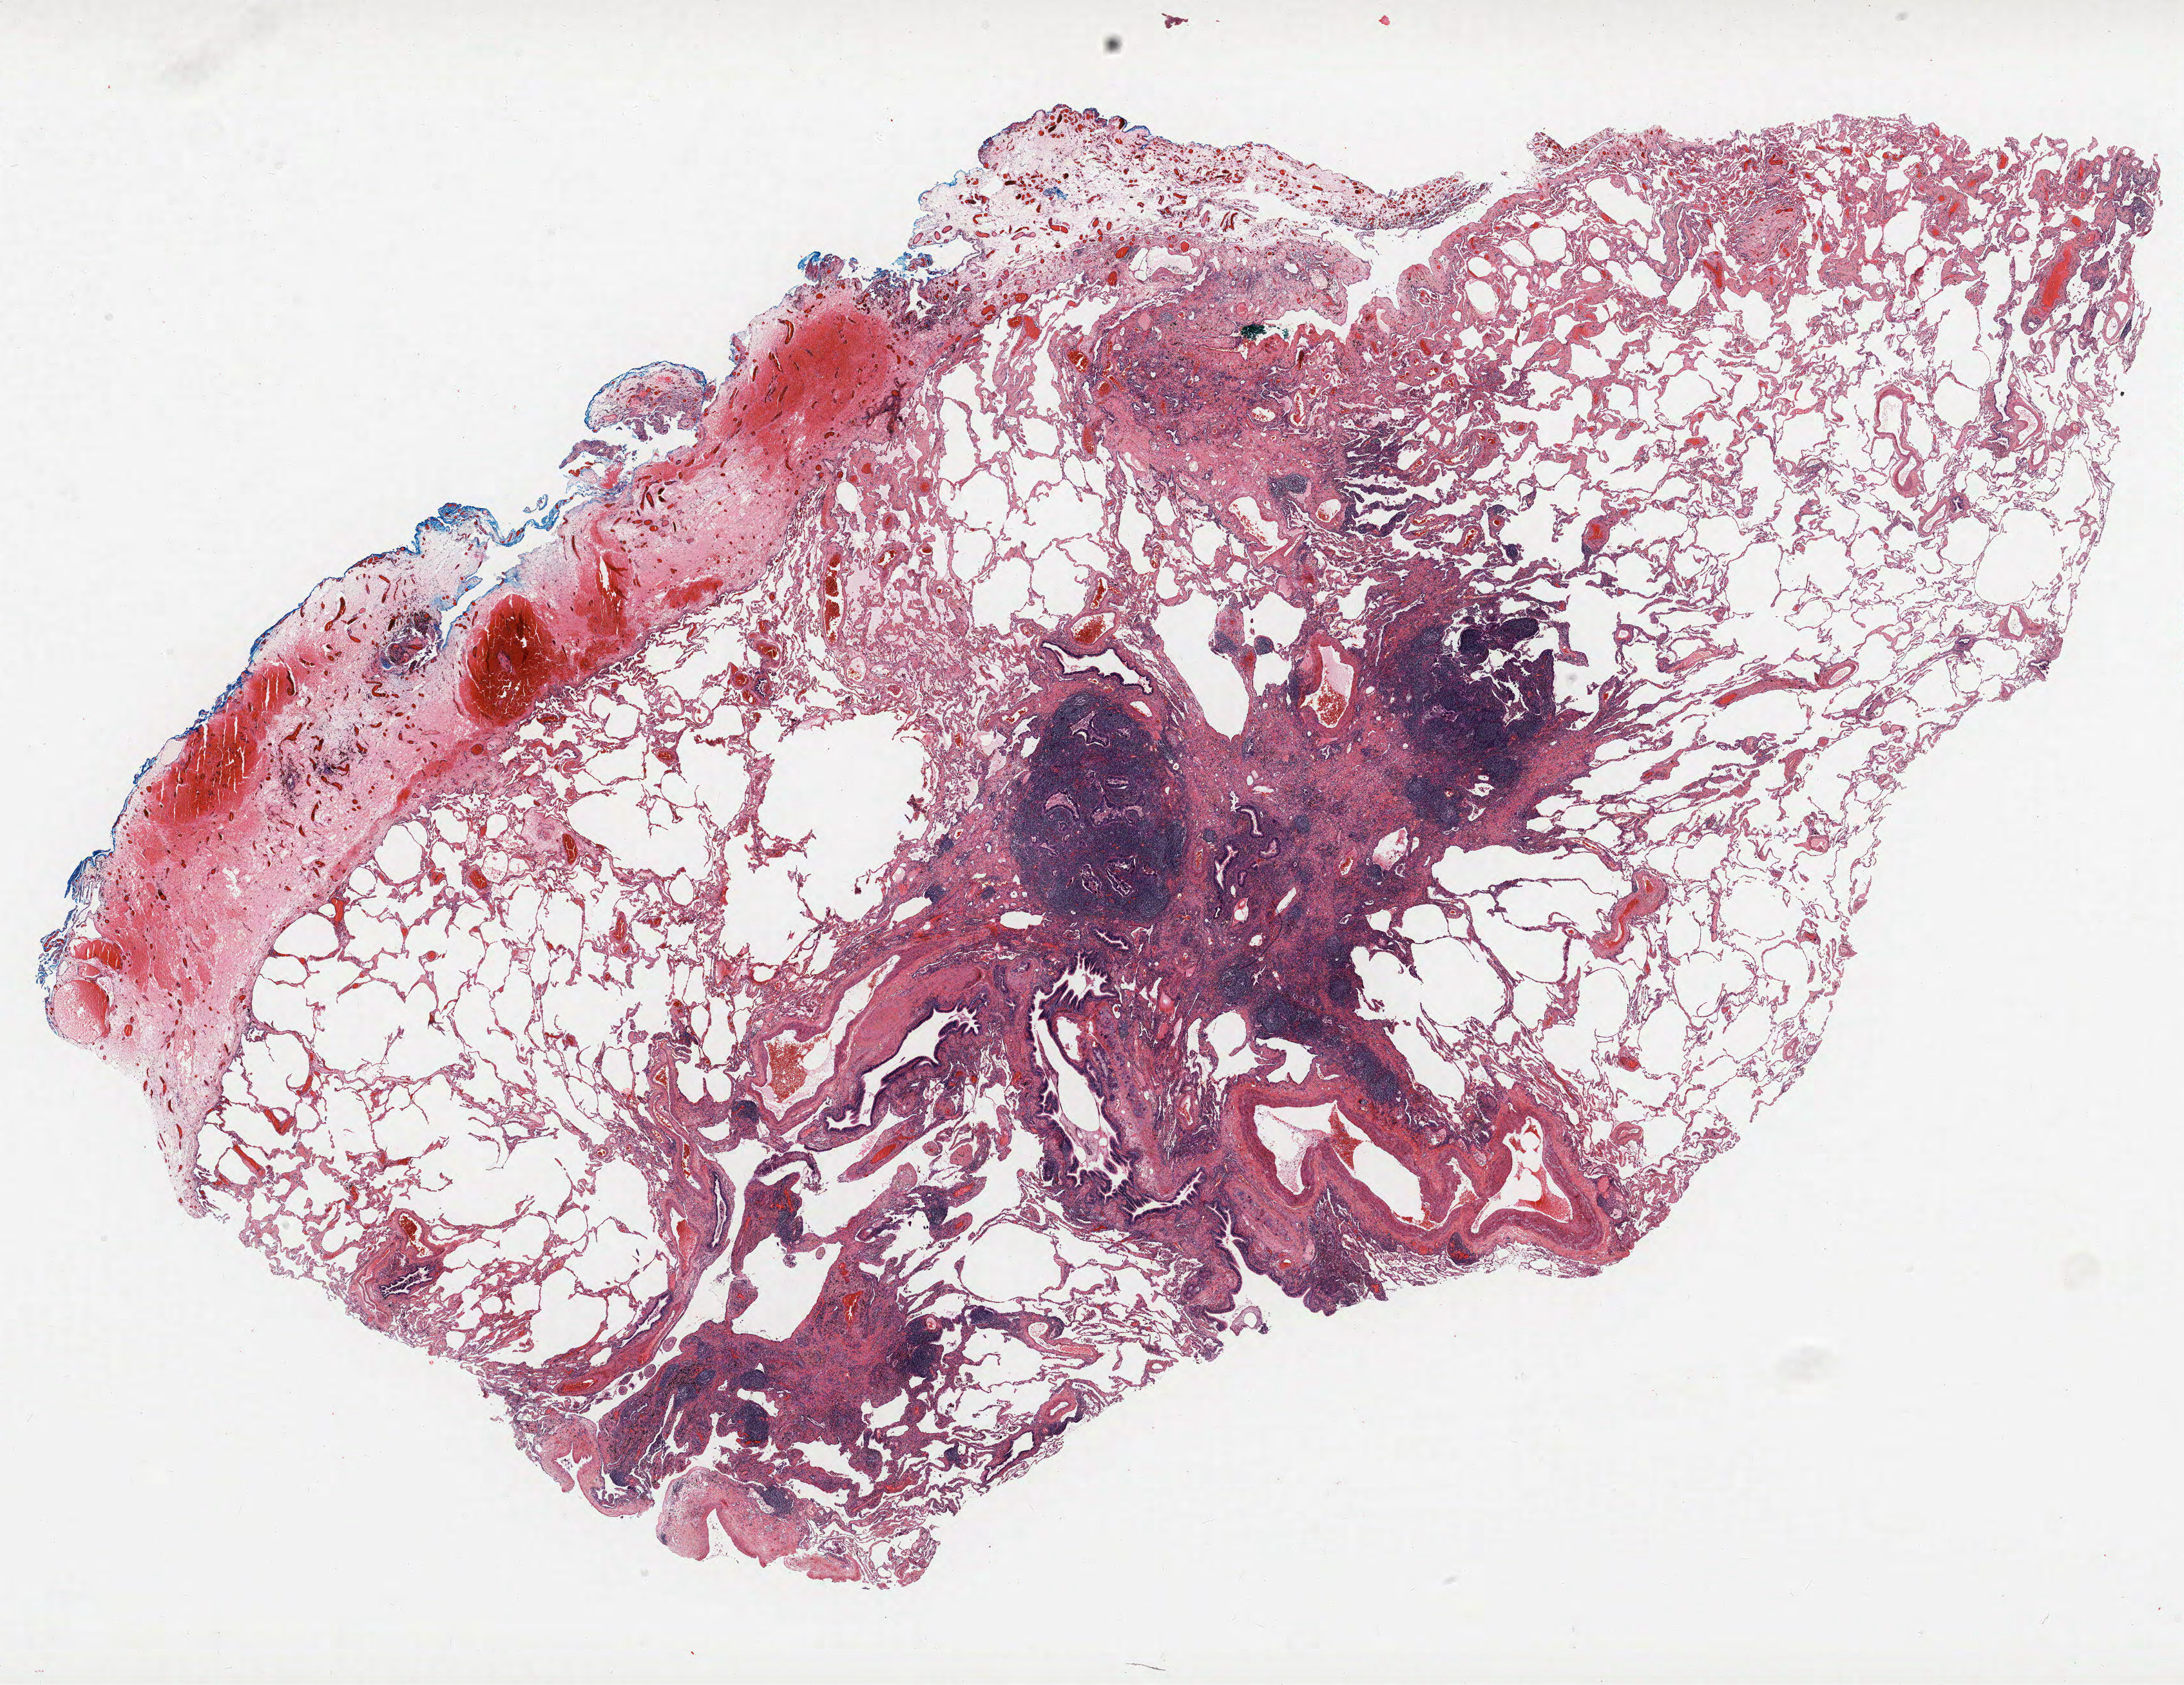
Whole-slide histology image, H&E, low-resolution overview of the scanned area, about 27.1 x 20.9 mm (acquisition: 40x scan), FFPE section, lung. Female, age 59 at enrolment. Current smoker at enrolment. Grade: poorly differentiated (G3).
- stage (AJCC 6th edition): IA
- participant's lung-cancer diagnosis: Adenocarcinoma, NOS (ICD-O-3 8140/3)
- ICD-O-3 topography: lower lobe of lung (C34.3)
- primary tumour location (clinical record): left lower lobe
- tumour size (pathology): 15 mm